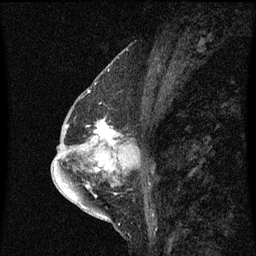
Breast MRI (dynamic contrast-enhanced), one sagittal slice; slice 33 of 60 in the series (ordered by position); dynamic contrast-enhanced series, image 2 of 3 at this slice position (ordered by acquisition); 1.5 T; TE 4.2 ms, TR 8.4 ms; 2 mm slice thickness; 256 × 256 image matrix. Female patient, age 57 years. Case-level facts recorded for this patient, not image findings: setting: breast cancer imaged before/during neoadjuvant chemotherapy; receptor status: HR-positive, HER2-negative.
Structures marked on this image (semi-automatic segmentation, software-assisted and operator-edited):
- analysis volume of interest (the breast-tissue region the enhancement analysis was run in; not a lesion): bounding box [x1, y1, x2, y2] px = [87, 120, 128, 145]
- tumour enhancement mask (voxels above the 70 % enhancement threshold inside the analysis volume of interest): [93, 120, 117, 145]